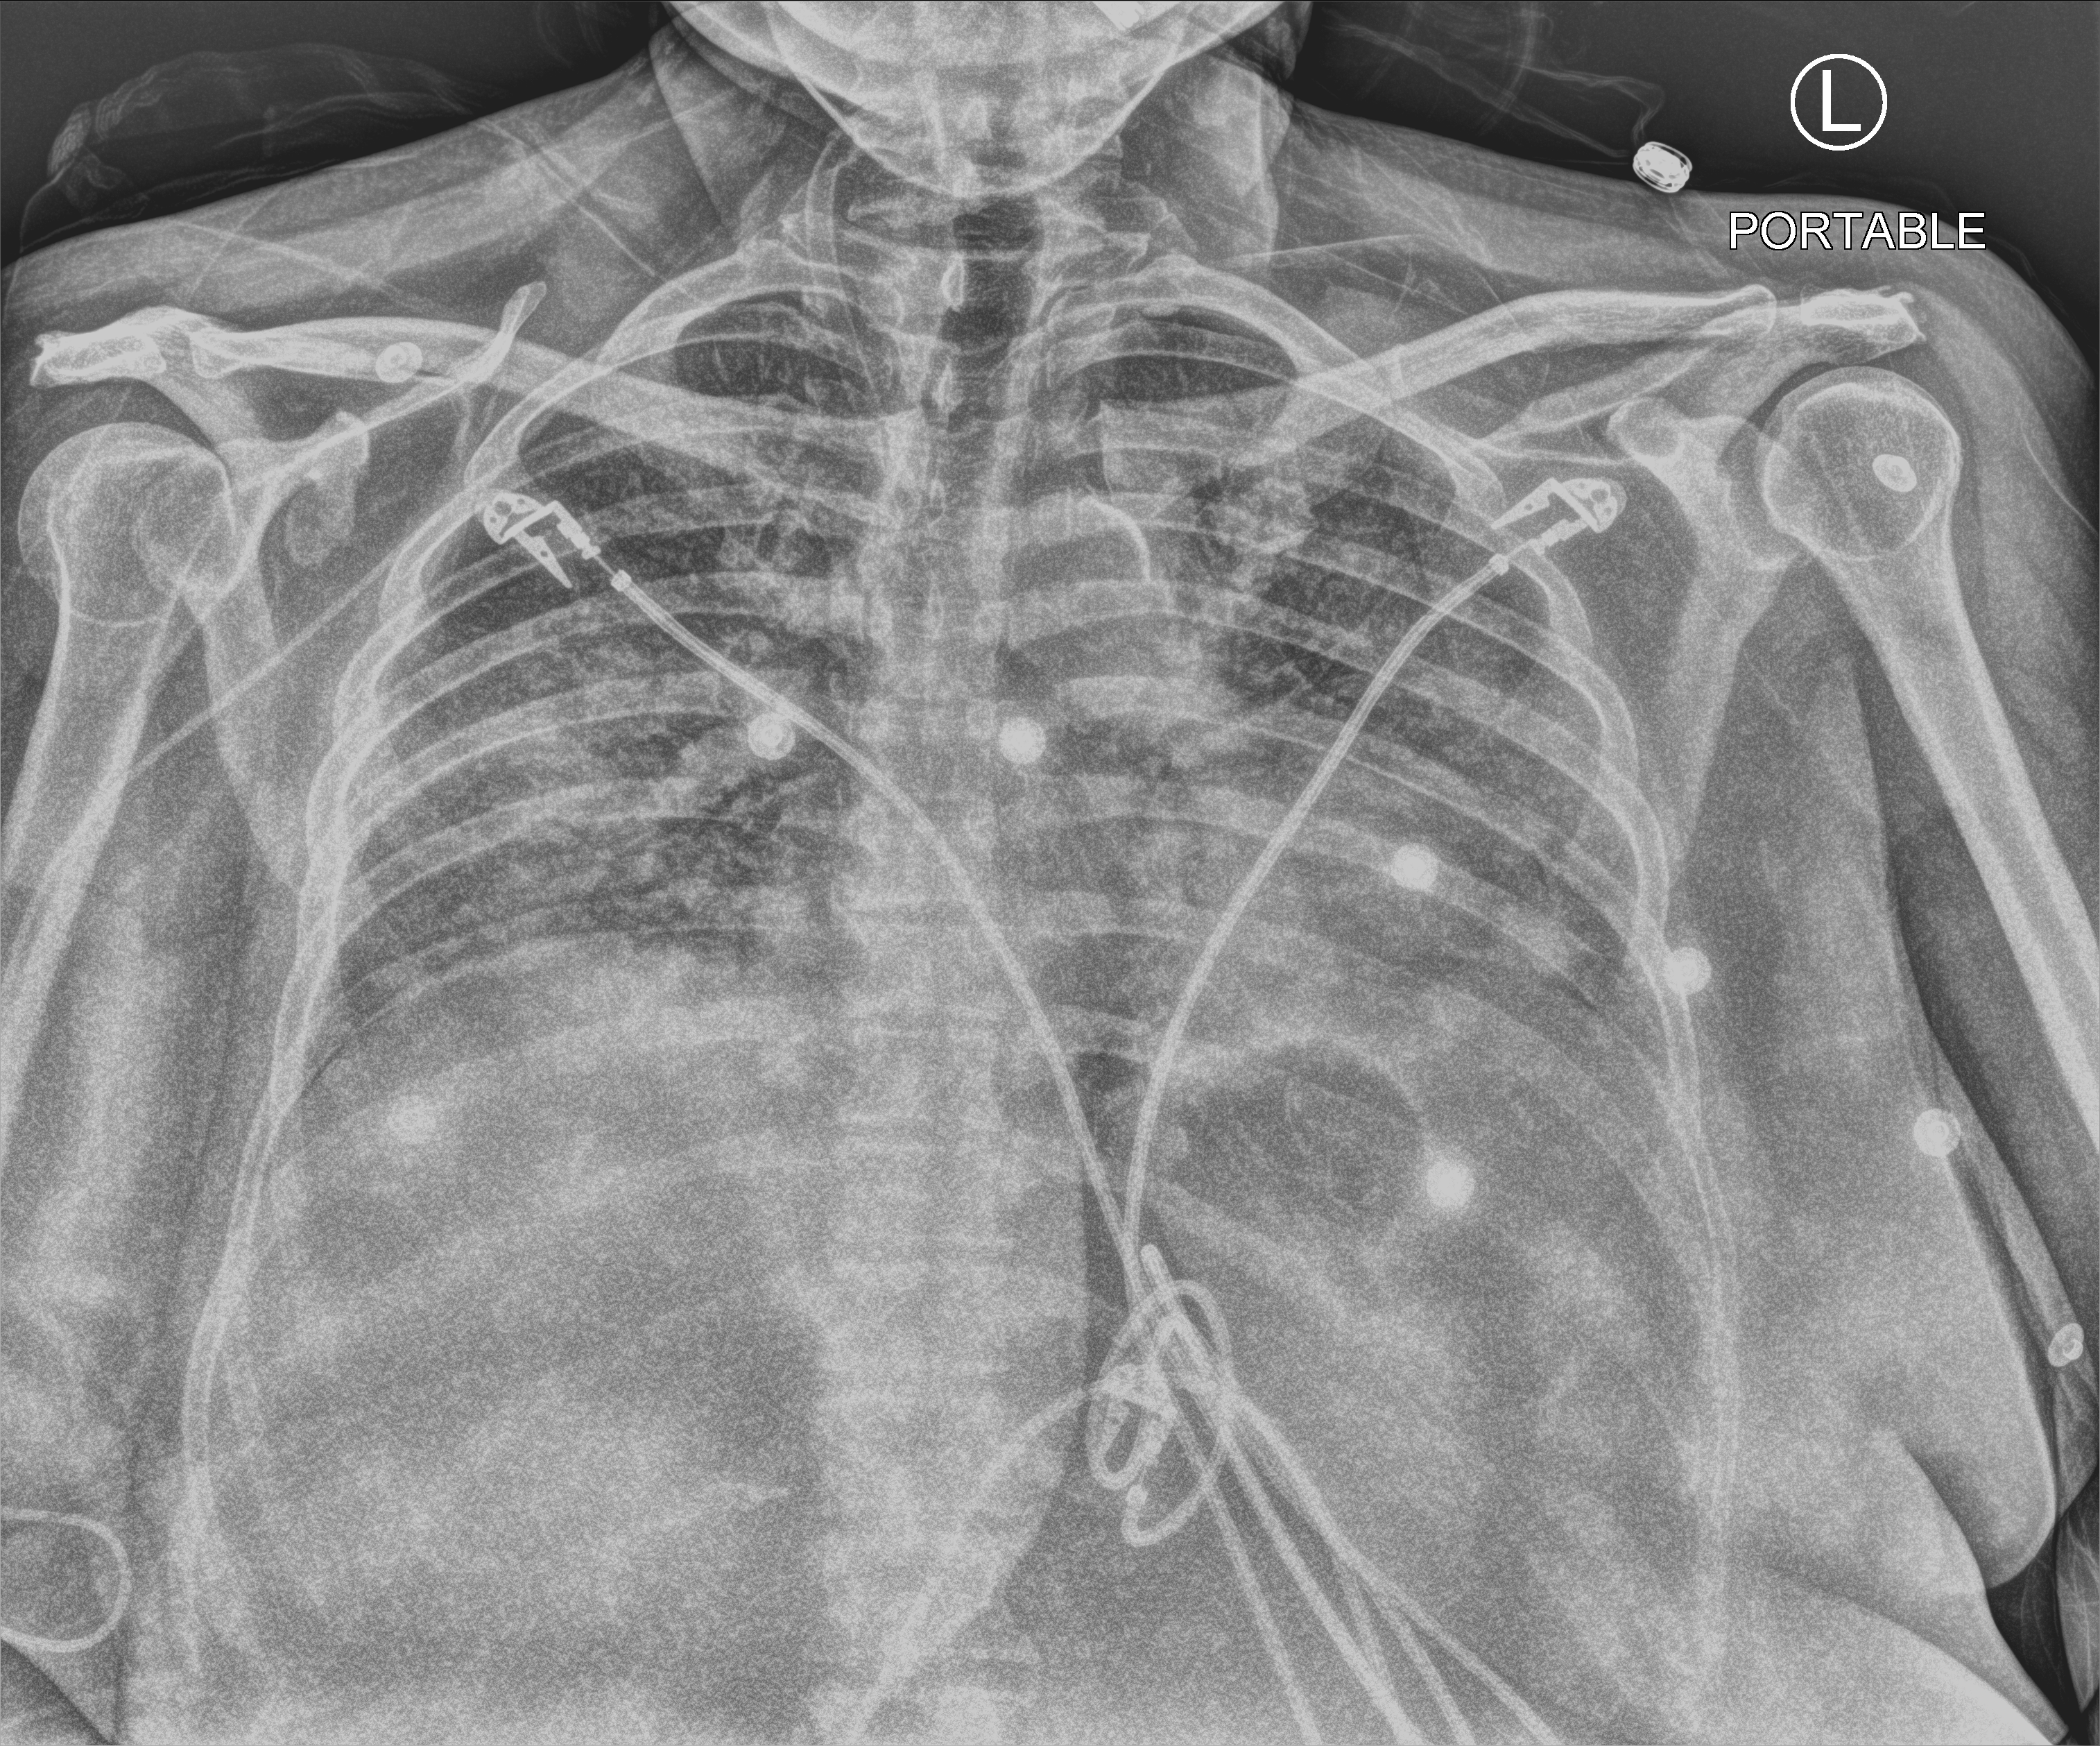
Chest X-ray (portable); anteroposterior (AP) projection. Patient hospitalised with COVID-19; female, aged 18–59 years.
From the hospital-stay record, not from the radiograph (when in the stay this image was taken is not recorded):
- smoking status (admission record): never
- mechanically ventilated during this hospital stay: no